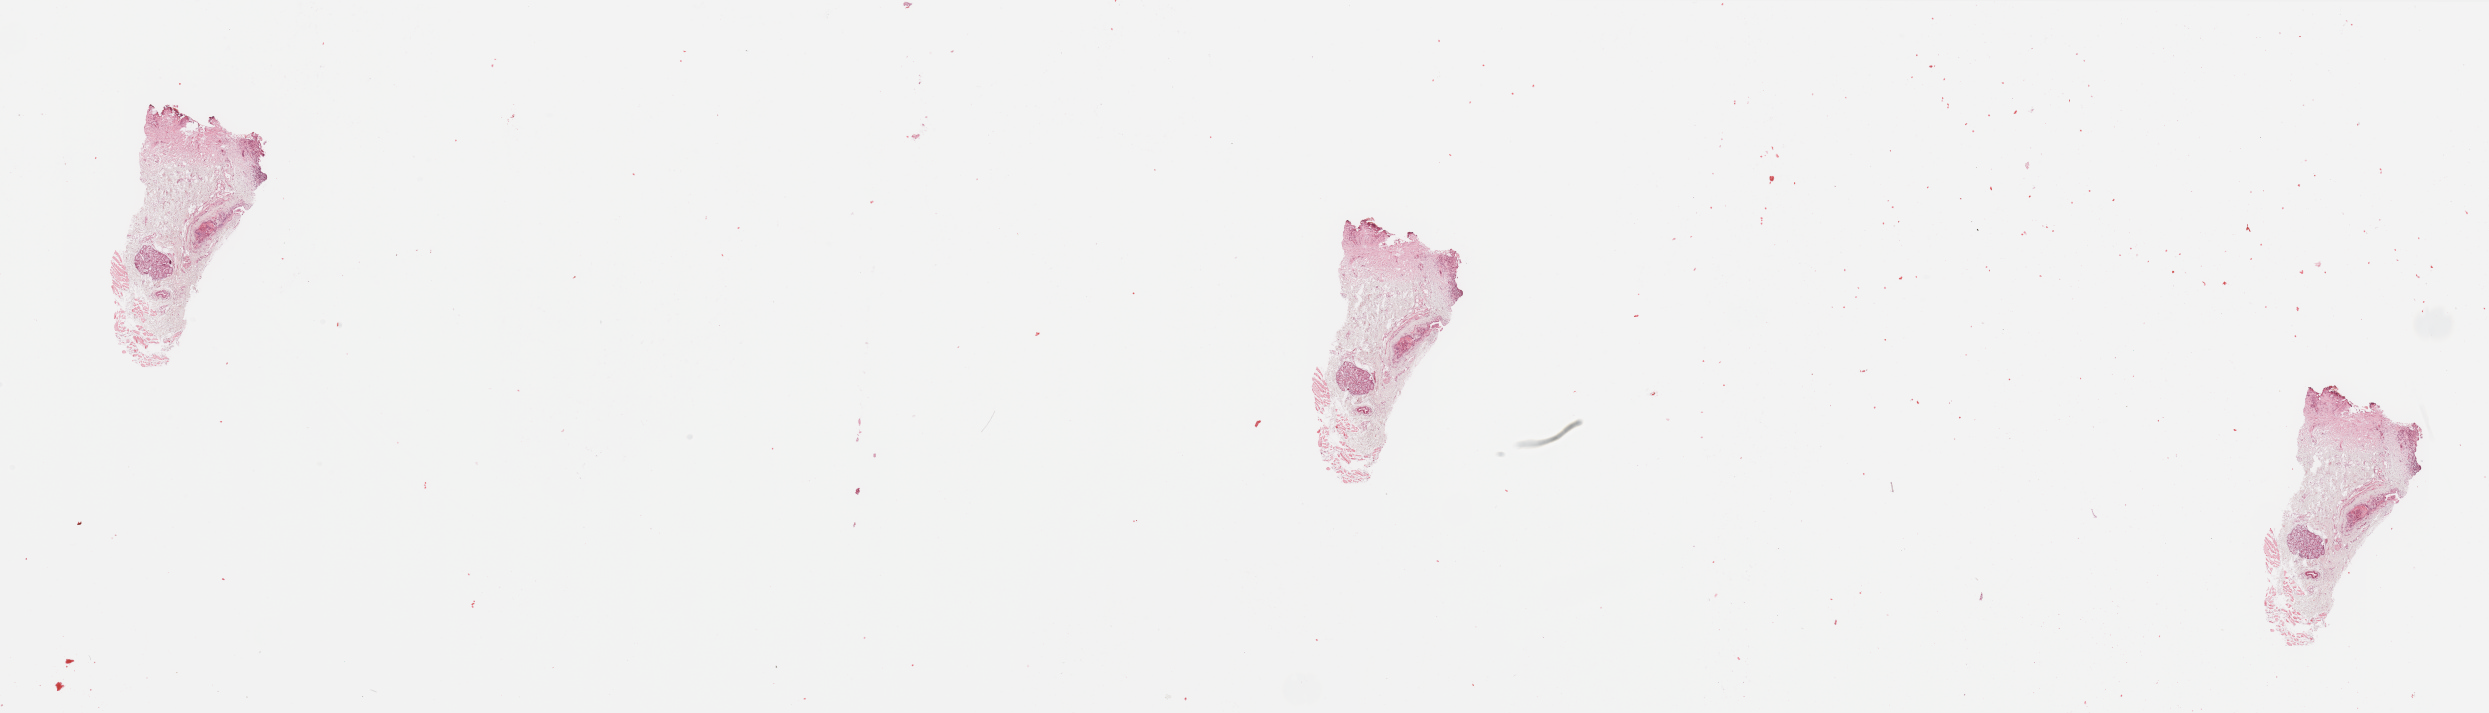
Hematoxylin and eosin (H&E) stained whole-slide image — whole scanned area (about 39.4 x 11.3 mm, from a 20x scan) shown as a low-resolution overview; head and neck, tissue type not recorded. Male, 45 y/o.
• patient diagnosis: Squamous cell carcinoma, NOS (floor of mouth, NOS)